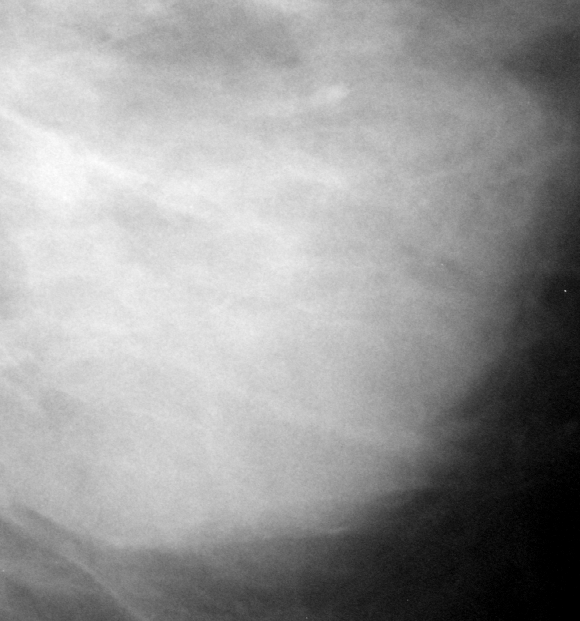
Region of interest cut from a scanned film mammogram (one marked finding), left breast, MLO view.
- Marked abnormality: mass, shape oval, margins ill defined; BI-RADS assessment category 3; pathology result (as recorded, not read from the image): benign.